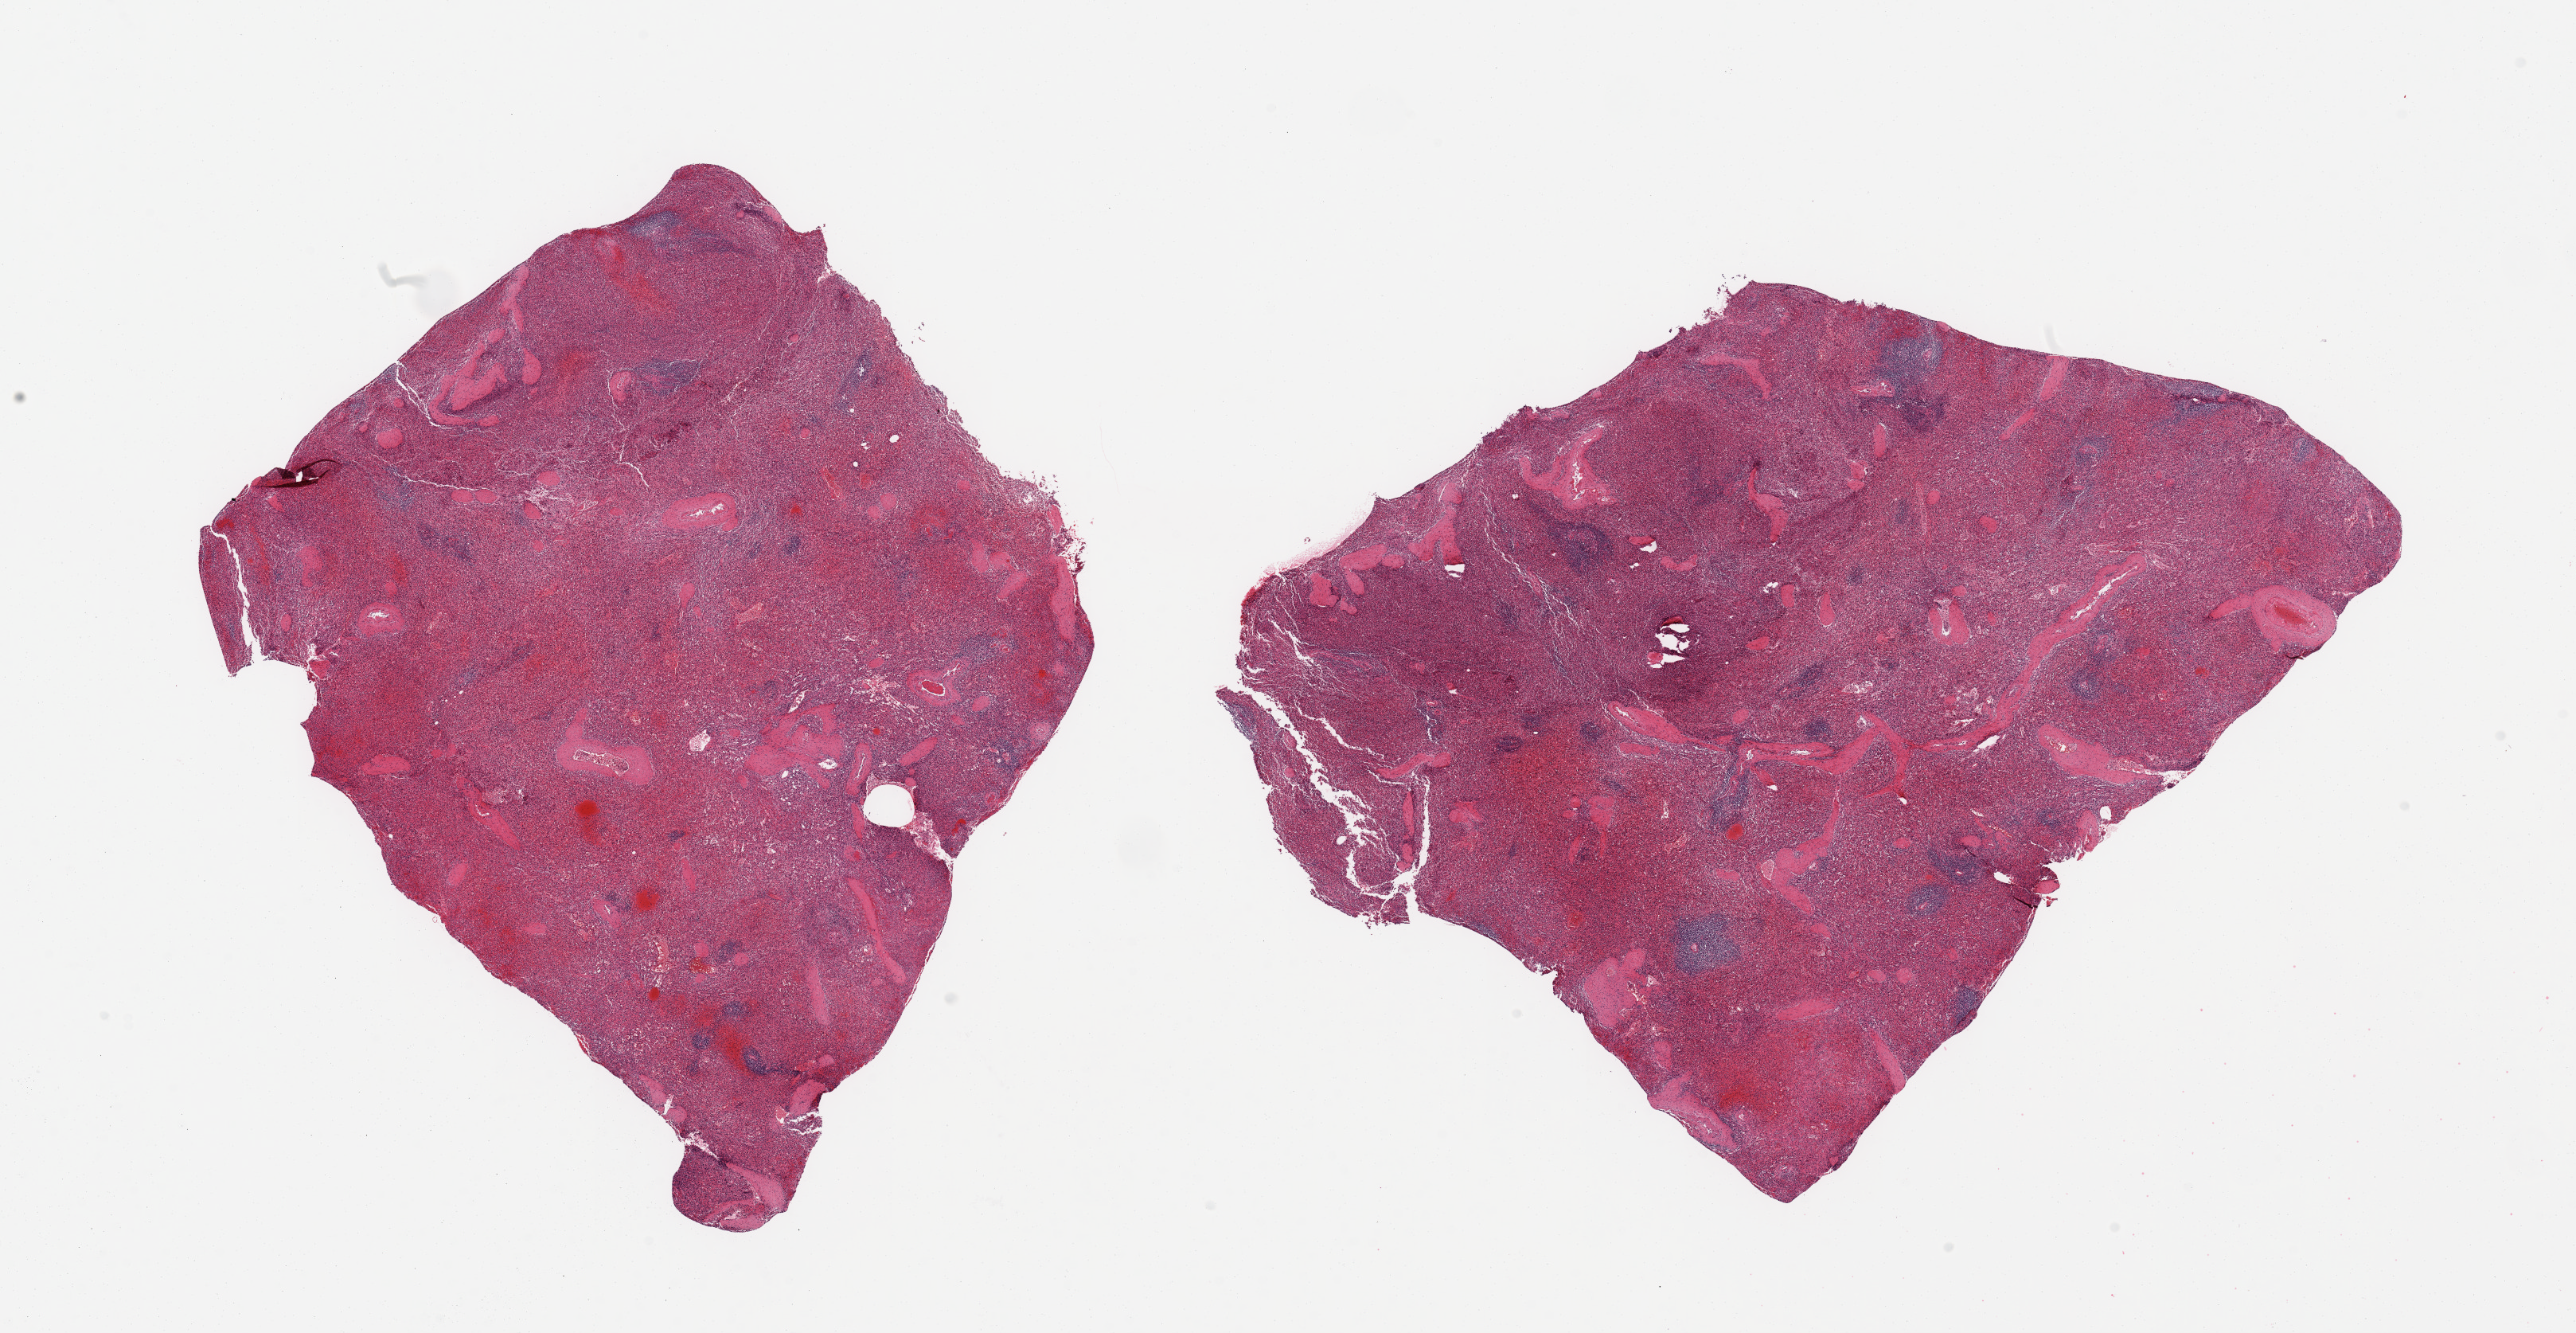
Digitized H&E-stained section, whole scanned area (about 25.6 x 13.2 mm, from a 20x scan) shown as a low-resolution overview. PAXgene-fixed paraffin-embedded (PFPE) section. Sampled site (target tissue): spleen. Donor tissue sample. Female donor.
Review note (as recorded): 2 pieces; focally moderate congestion.